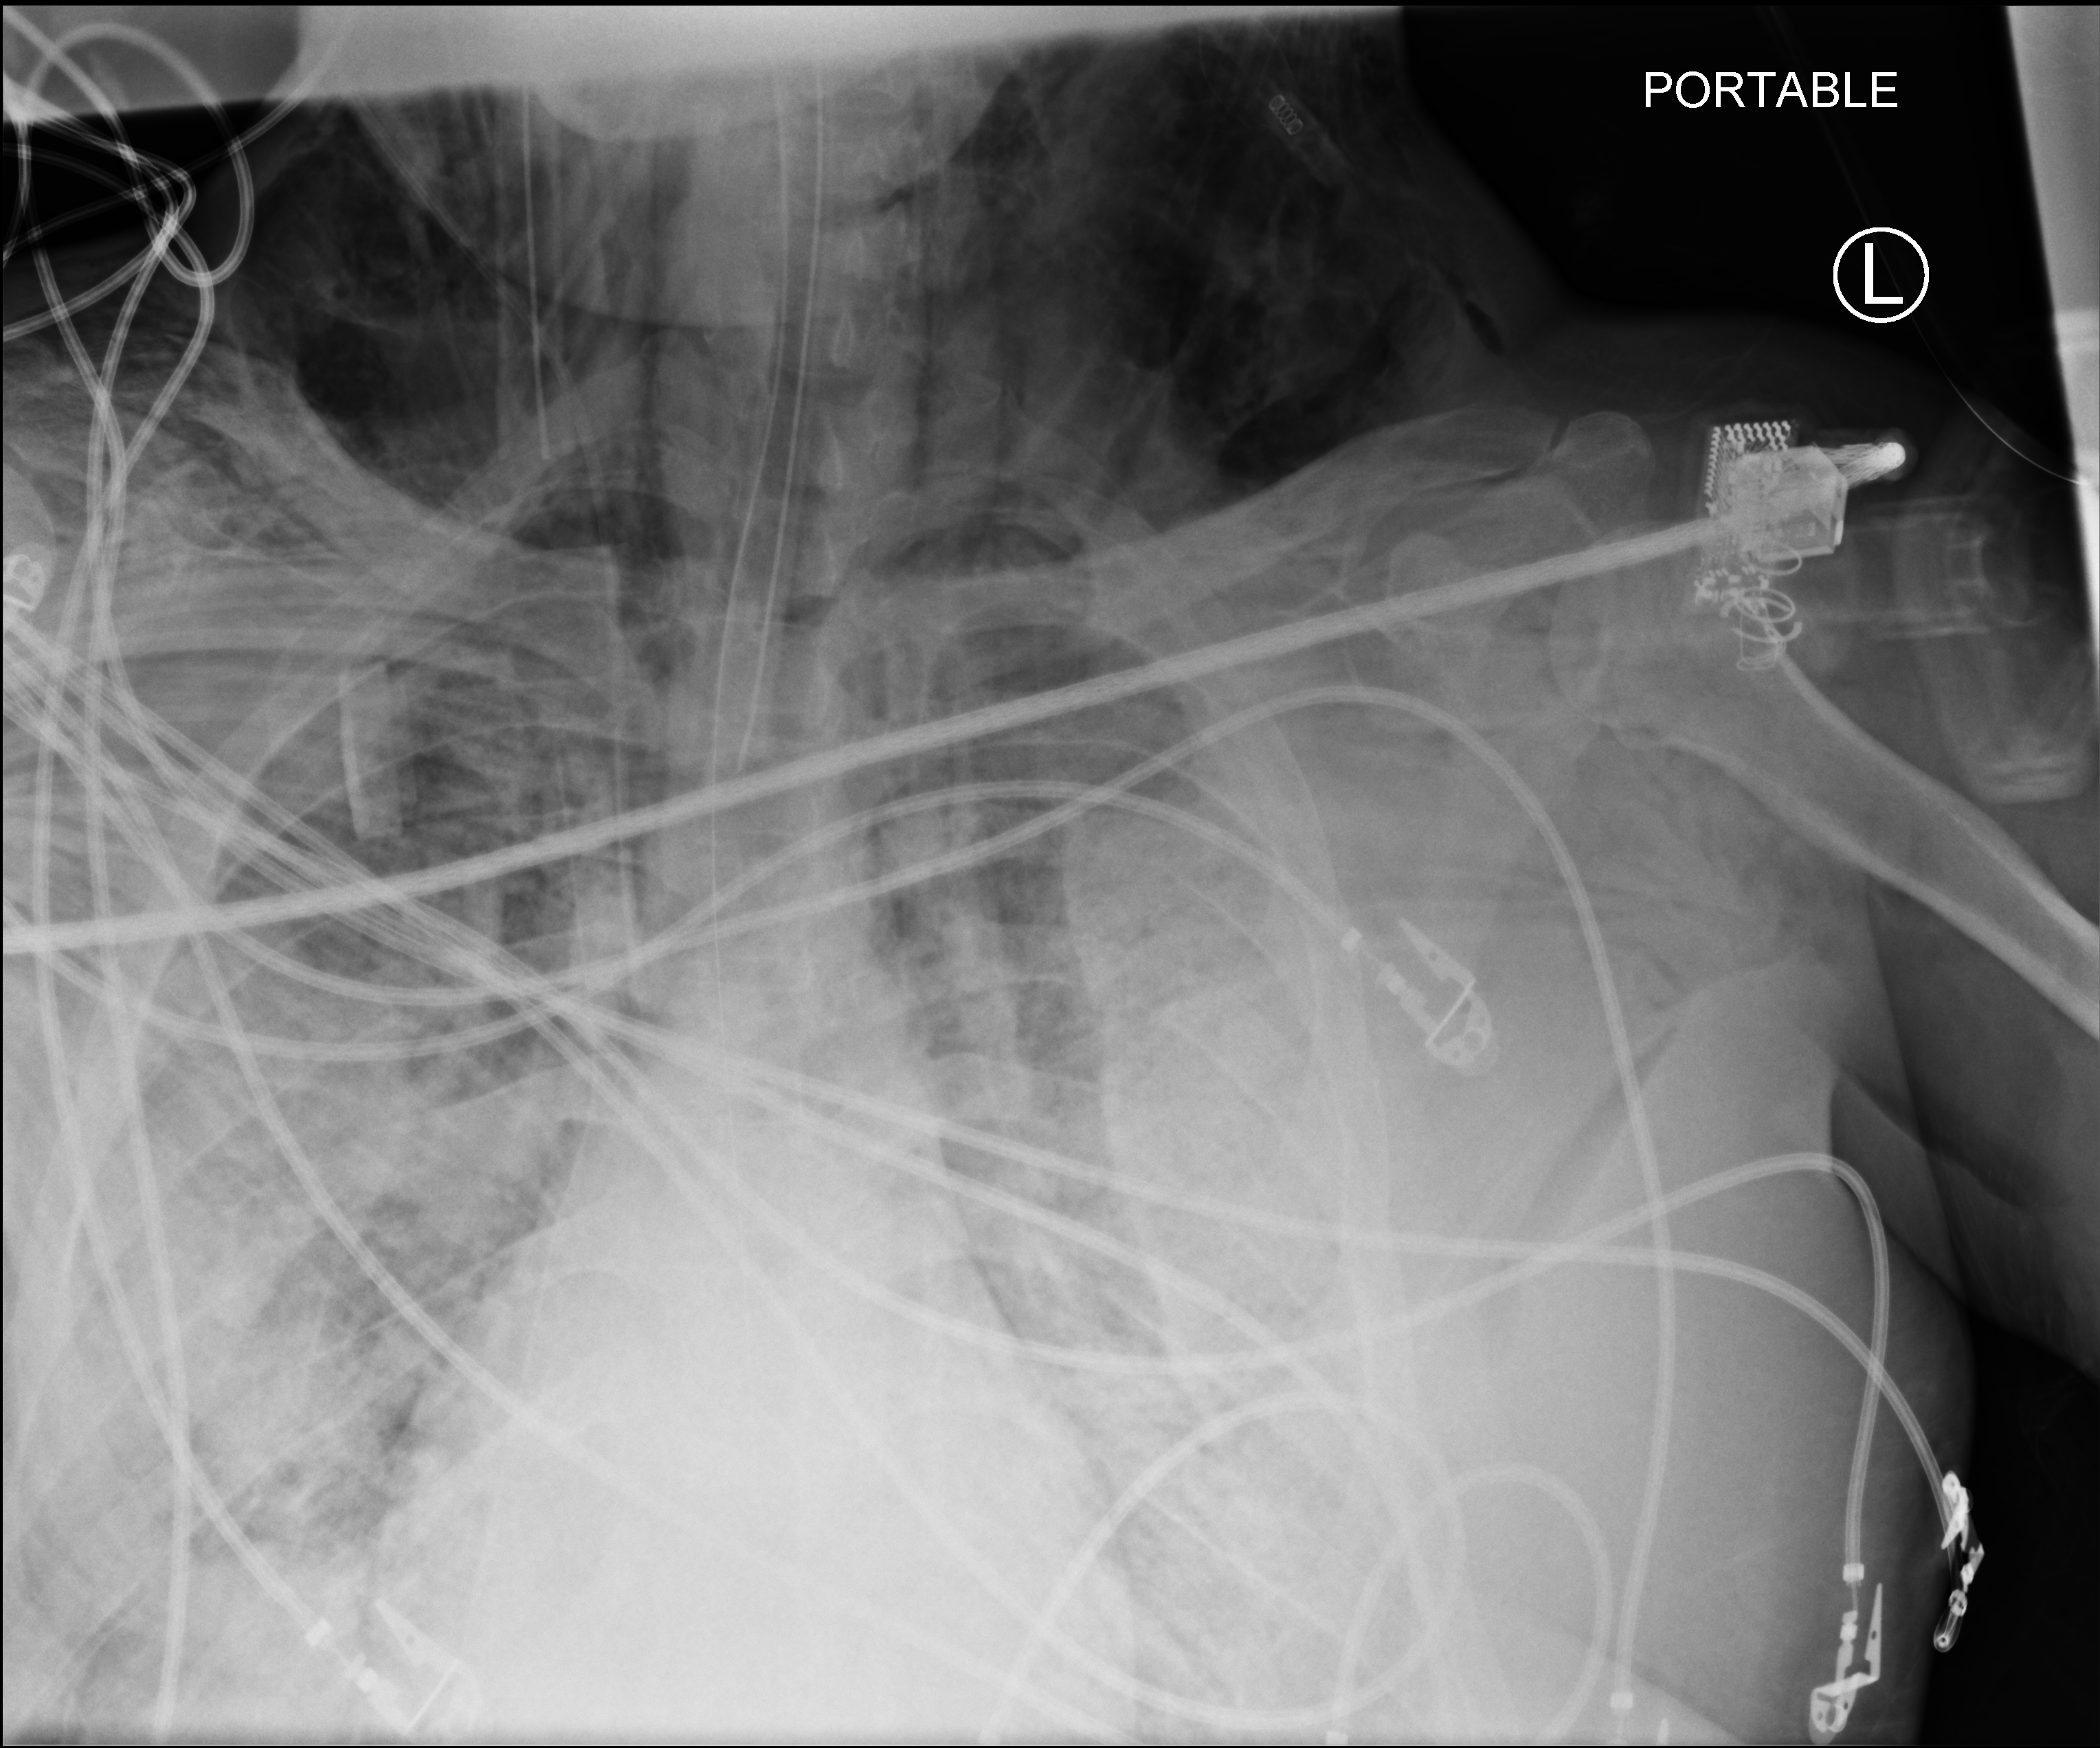
Chest X-ray (portable), anteroposterior (AP) projection. Patient hospitalised with COVID-19, aged 18–59 years.
From the hospital-stay record, not from the radiograph (when in the stay this image was taken is not recorded): mechanically ventilated during this hospital stay: yes; length of hospital stay: 15 days; COPD (admission record): no.